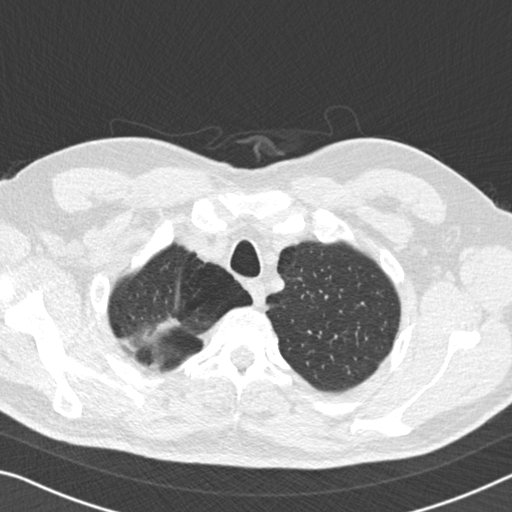
Chest CT (low-dose screening protocol), one axial image; third screening round (two years after baseline); lung window (W 1500 / L -600 HU); standard (soft-tissue) reconstruction kernel (B30f); 512 × 512 image matrix, field of view 336 × 336 mm. Male, age 56 years at enrolment.
Expert reader's lesion annotation, box from (x=136, y=305) to (x=200, y=360) px. The exam's reader record, not a measurement of the box and not confirmed to be the same lesion: non-calcified nodule or mass ≥4 mm, right upper lobe, 13 × 13 mm, spiculated (stellate) margins, soft tissue attenuation, pre-existing on the prior screen: yes; interval growth: yes. Lung cancer was diagnosed 97 days after this screen: adenocarcinoma, NOS, right upper lobe, moderately differentiated (G2), stage IA (AJCC 6th edition), 9 mm at pathology.